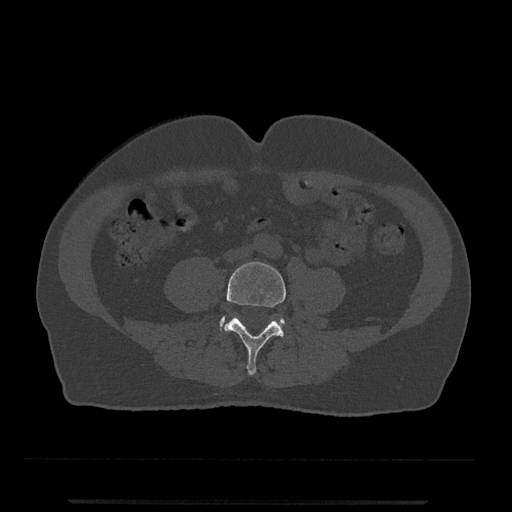
CT including the spine, one axial slice. Position 124 of 797 along the scan axis. Reconstruction kernel Br40s/3. 120 kVp. Bone window (W 1800 / L 400 HU). 0.5 mm slice thickness. 512 × 512 image matrix. Male patient, age 63 years. From the clinical record (not read from this slice): primary cancer: prostate.
Outlined on this slice (semi-automatically segmented with operator editing):
- L4 vertebra: bounding box [x1, y1, x2, y2] px = [224, 262, 286, 375]
- L5 vertebra: [219, 316, 284, 330]